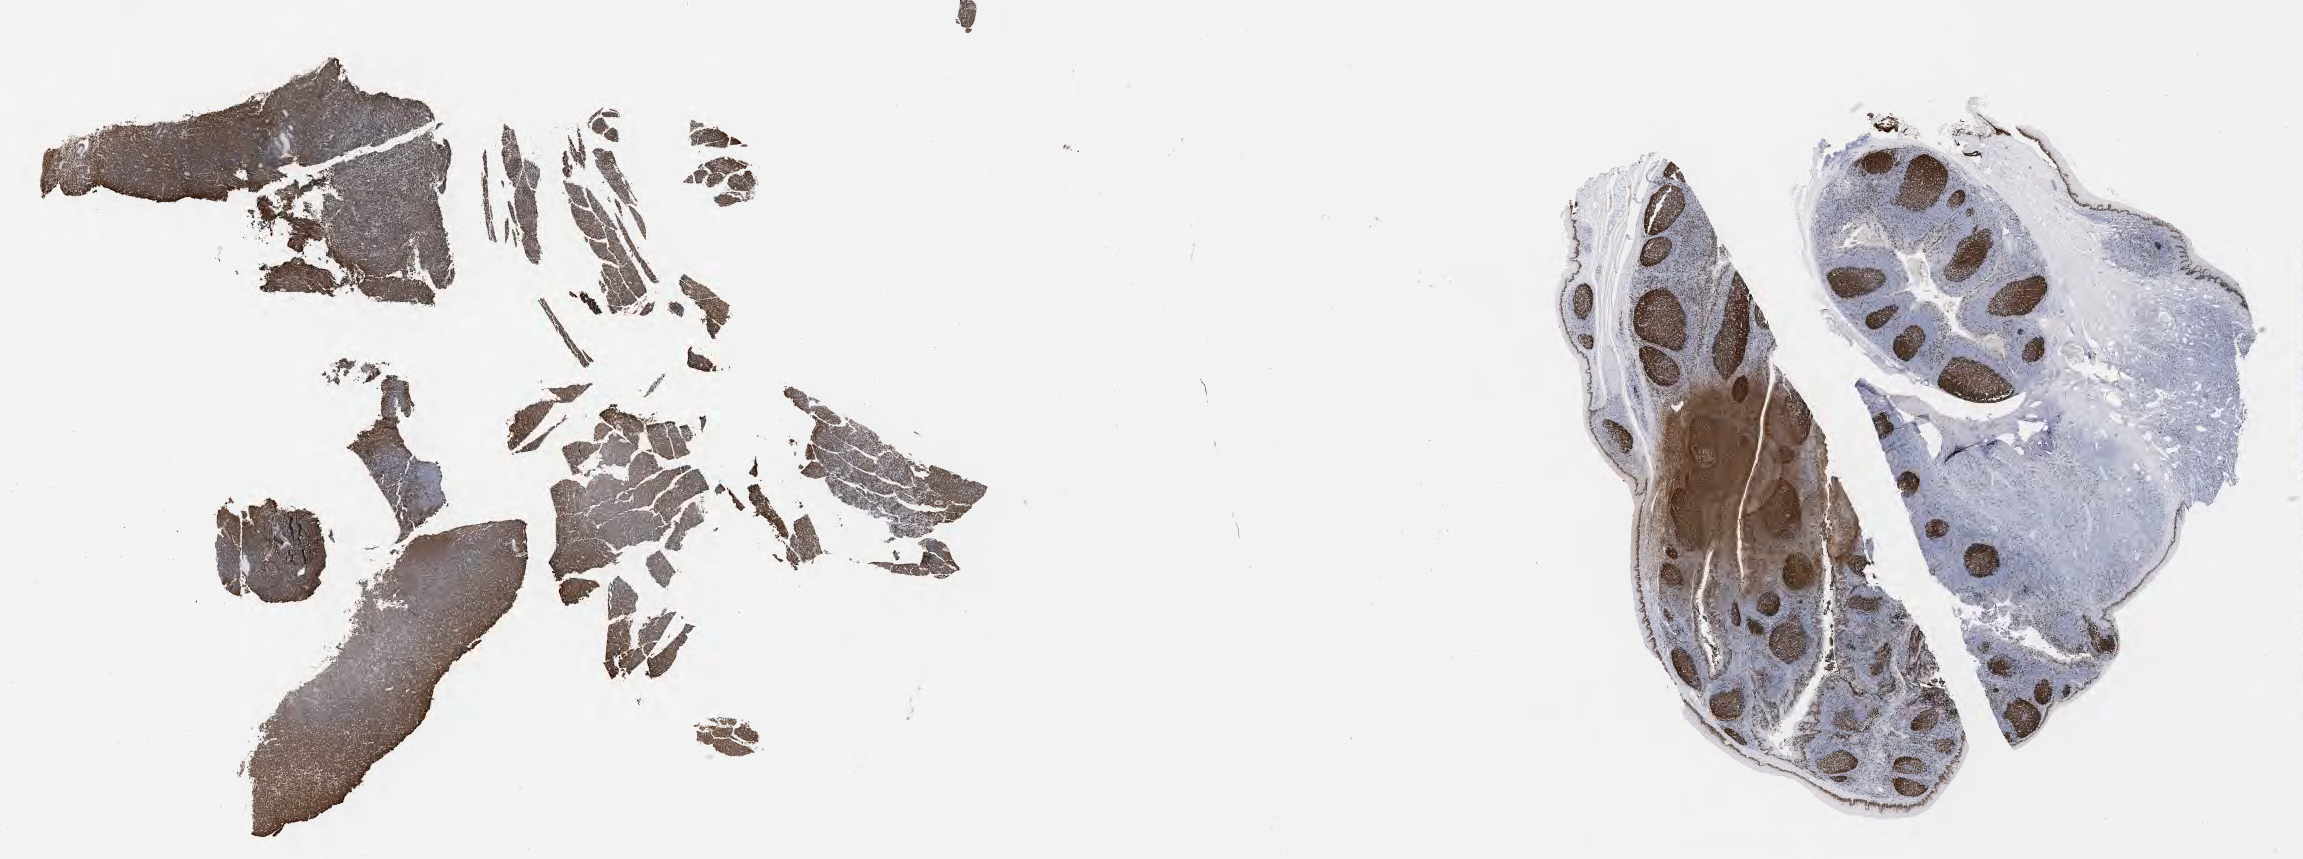
IHC for Ki-67, whole-slide image, low-resolution overview of the scanned area, about 37.2 x 13.9 mm. Tumor tissue. Male, age 9 years at initial diagnosis.
Histologic diagnosis: Burkitt lymphoma, NOS.